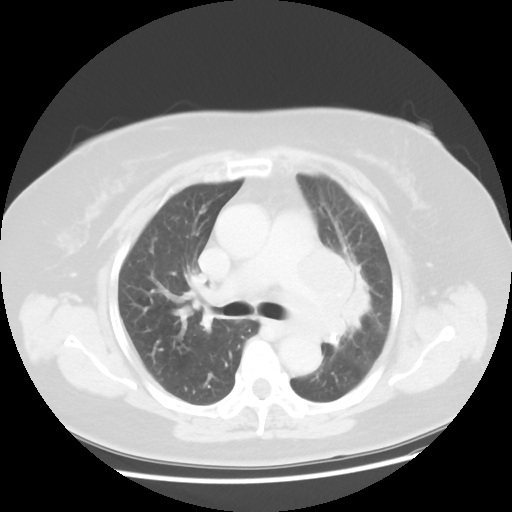
Chest CT, one axial slice; position 29 of 49 along the scan axis; lung window (W 1500 / L -600 HU); 5 mm slice thickness; 512 × 512 image matrix. Female patient, age 58 years. From the clinical record (not read from this slice): clinical TNM (as recorded): T4 N3 M0.
Outlined on this slice (rectangle marked by the reading radiologist):
- lung tumour (recorded histology: small cell carcinoma): bounding box <278,233,395,358> (left, top, right, bottom; pixels)